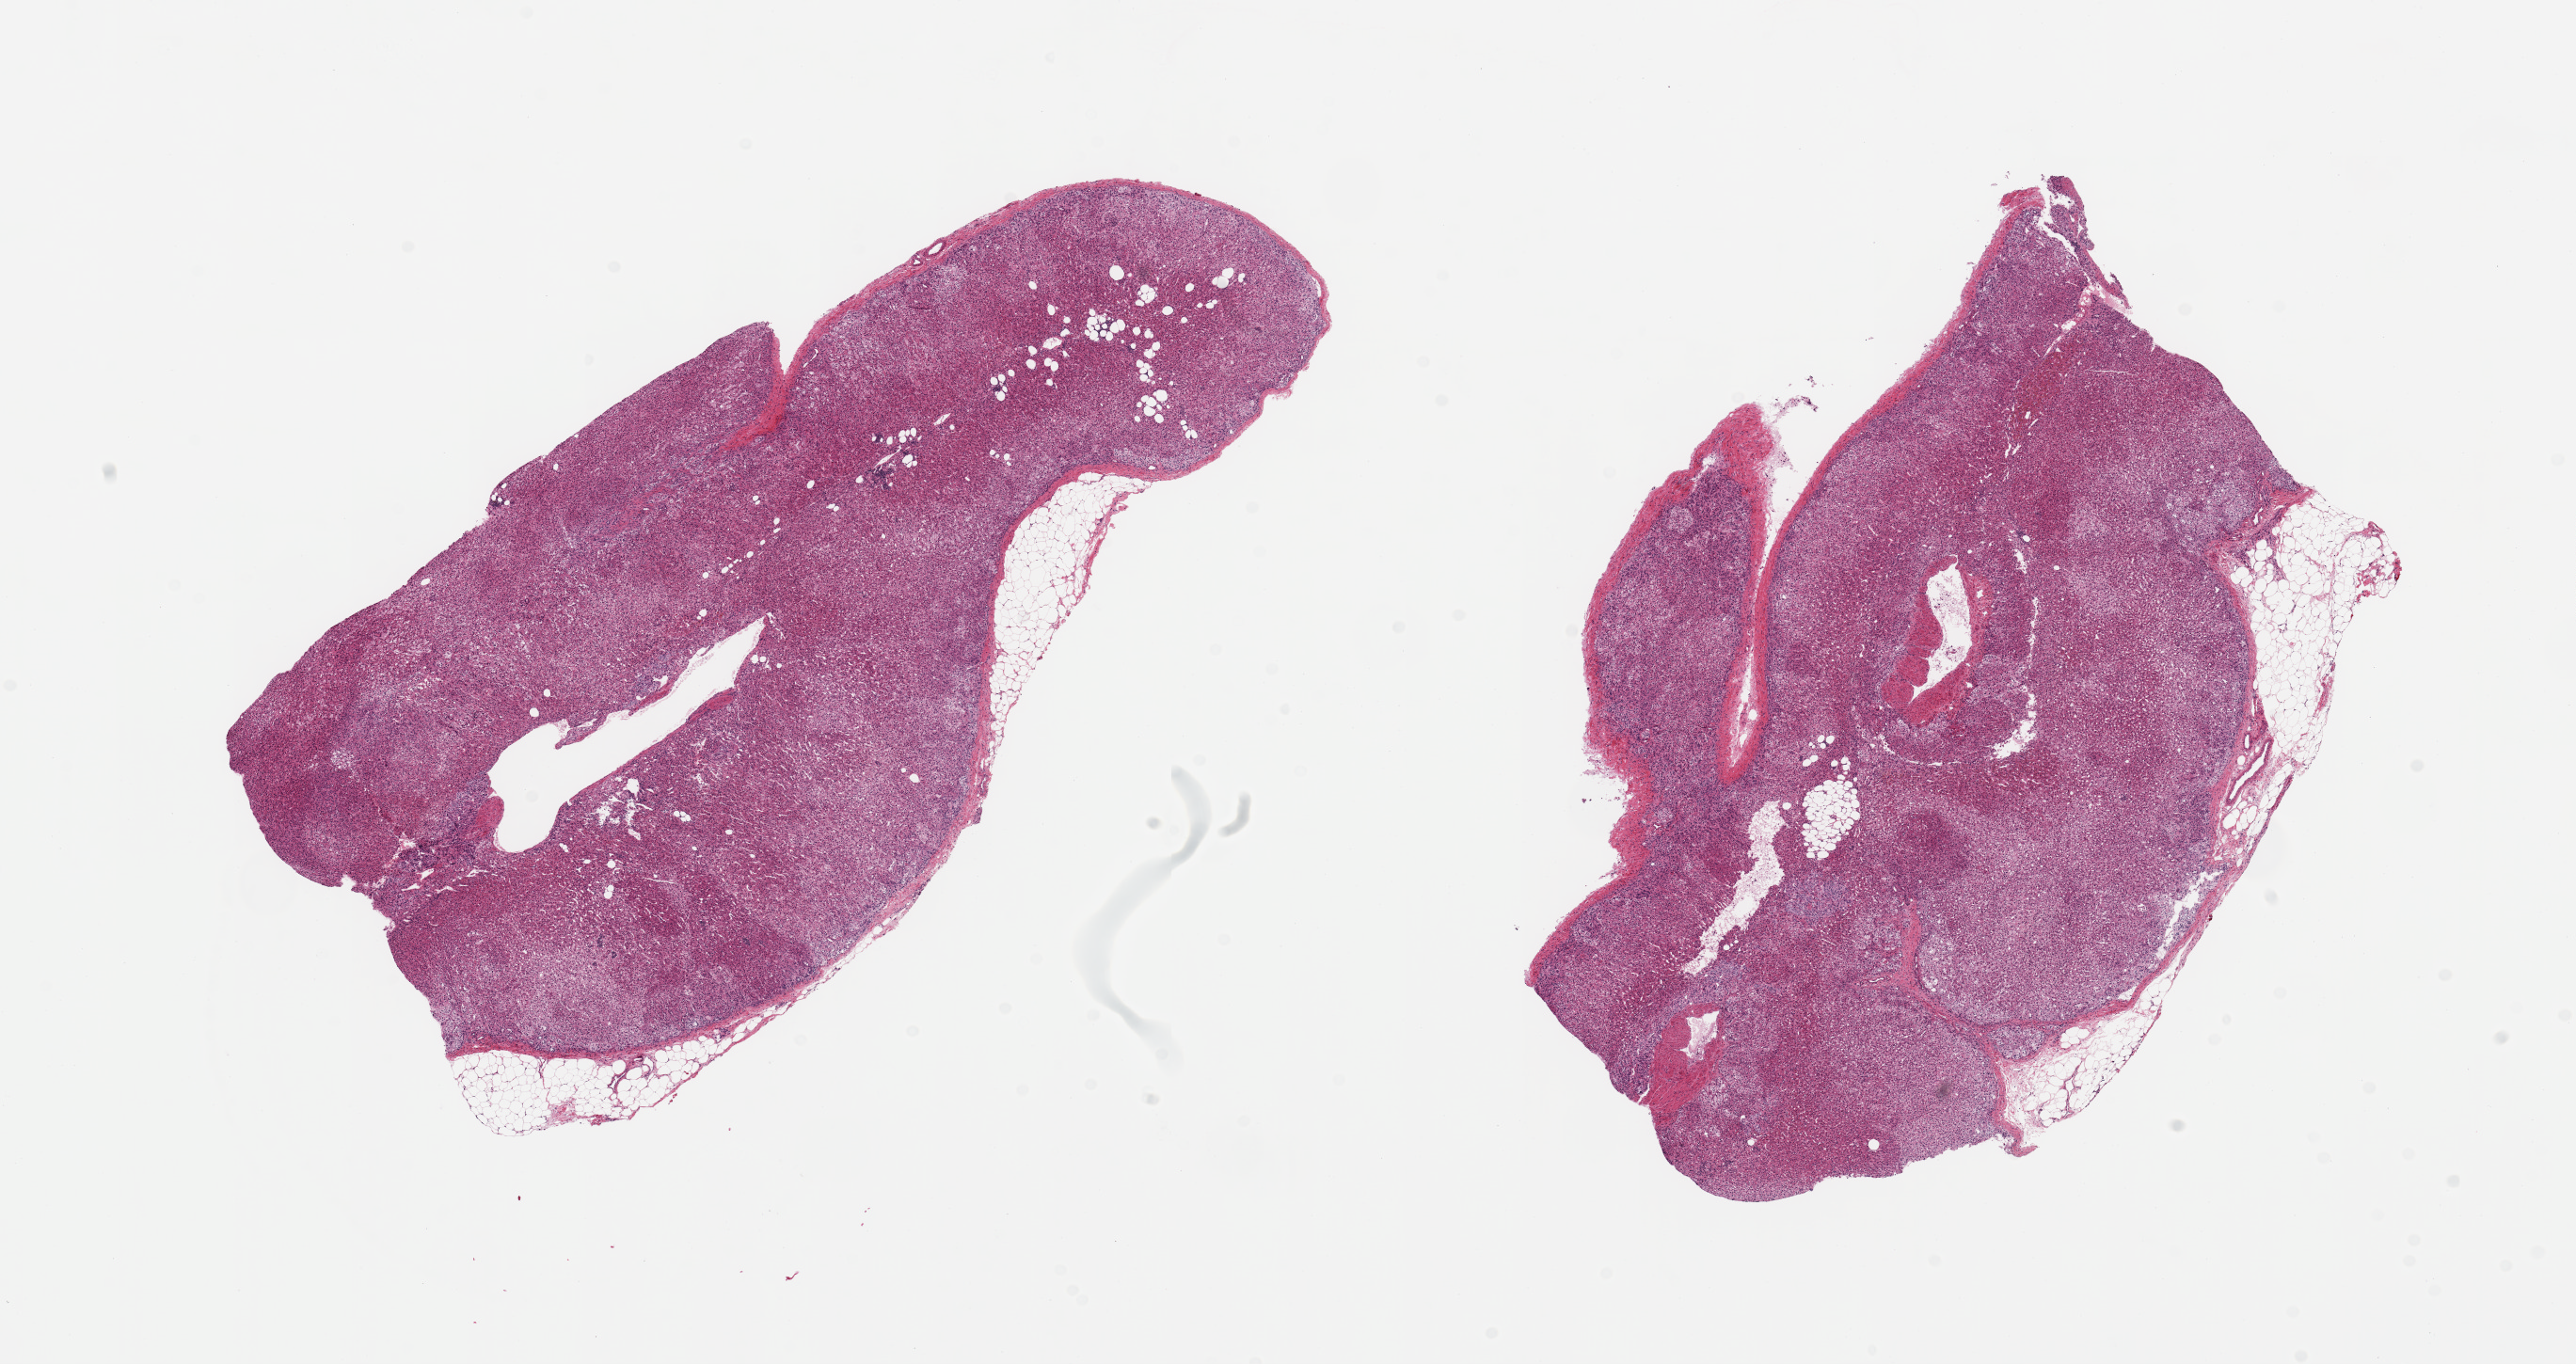
Hematoxylin and eosin (H&E) whole-slide image — low-resolution overview of the scanned area, about 21.7 x 11.5 mm; PAXgene-fixed paraffin-embedded (PFPE) section; target tissue: adrenal gland; donor tissue sample. Female donor.
Reviewer comment on this tissue sample: 2 ~9x5mm pieces, well-preserved.